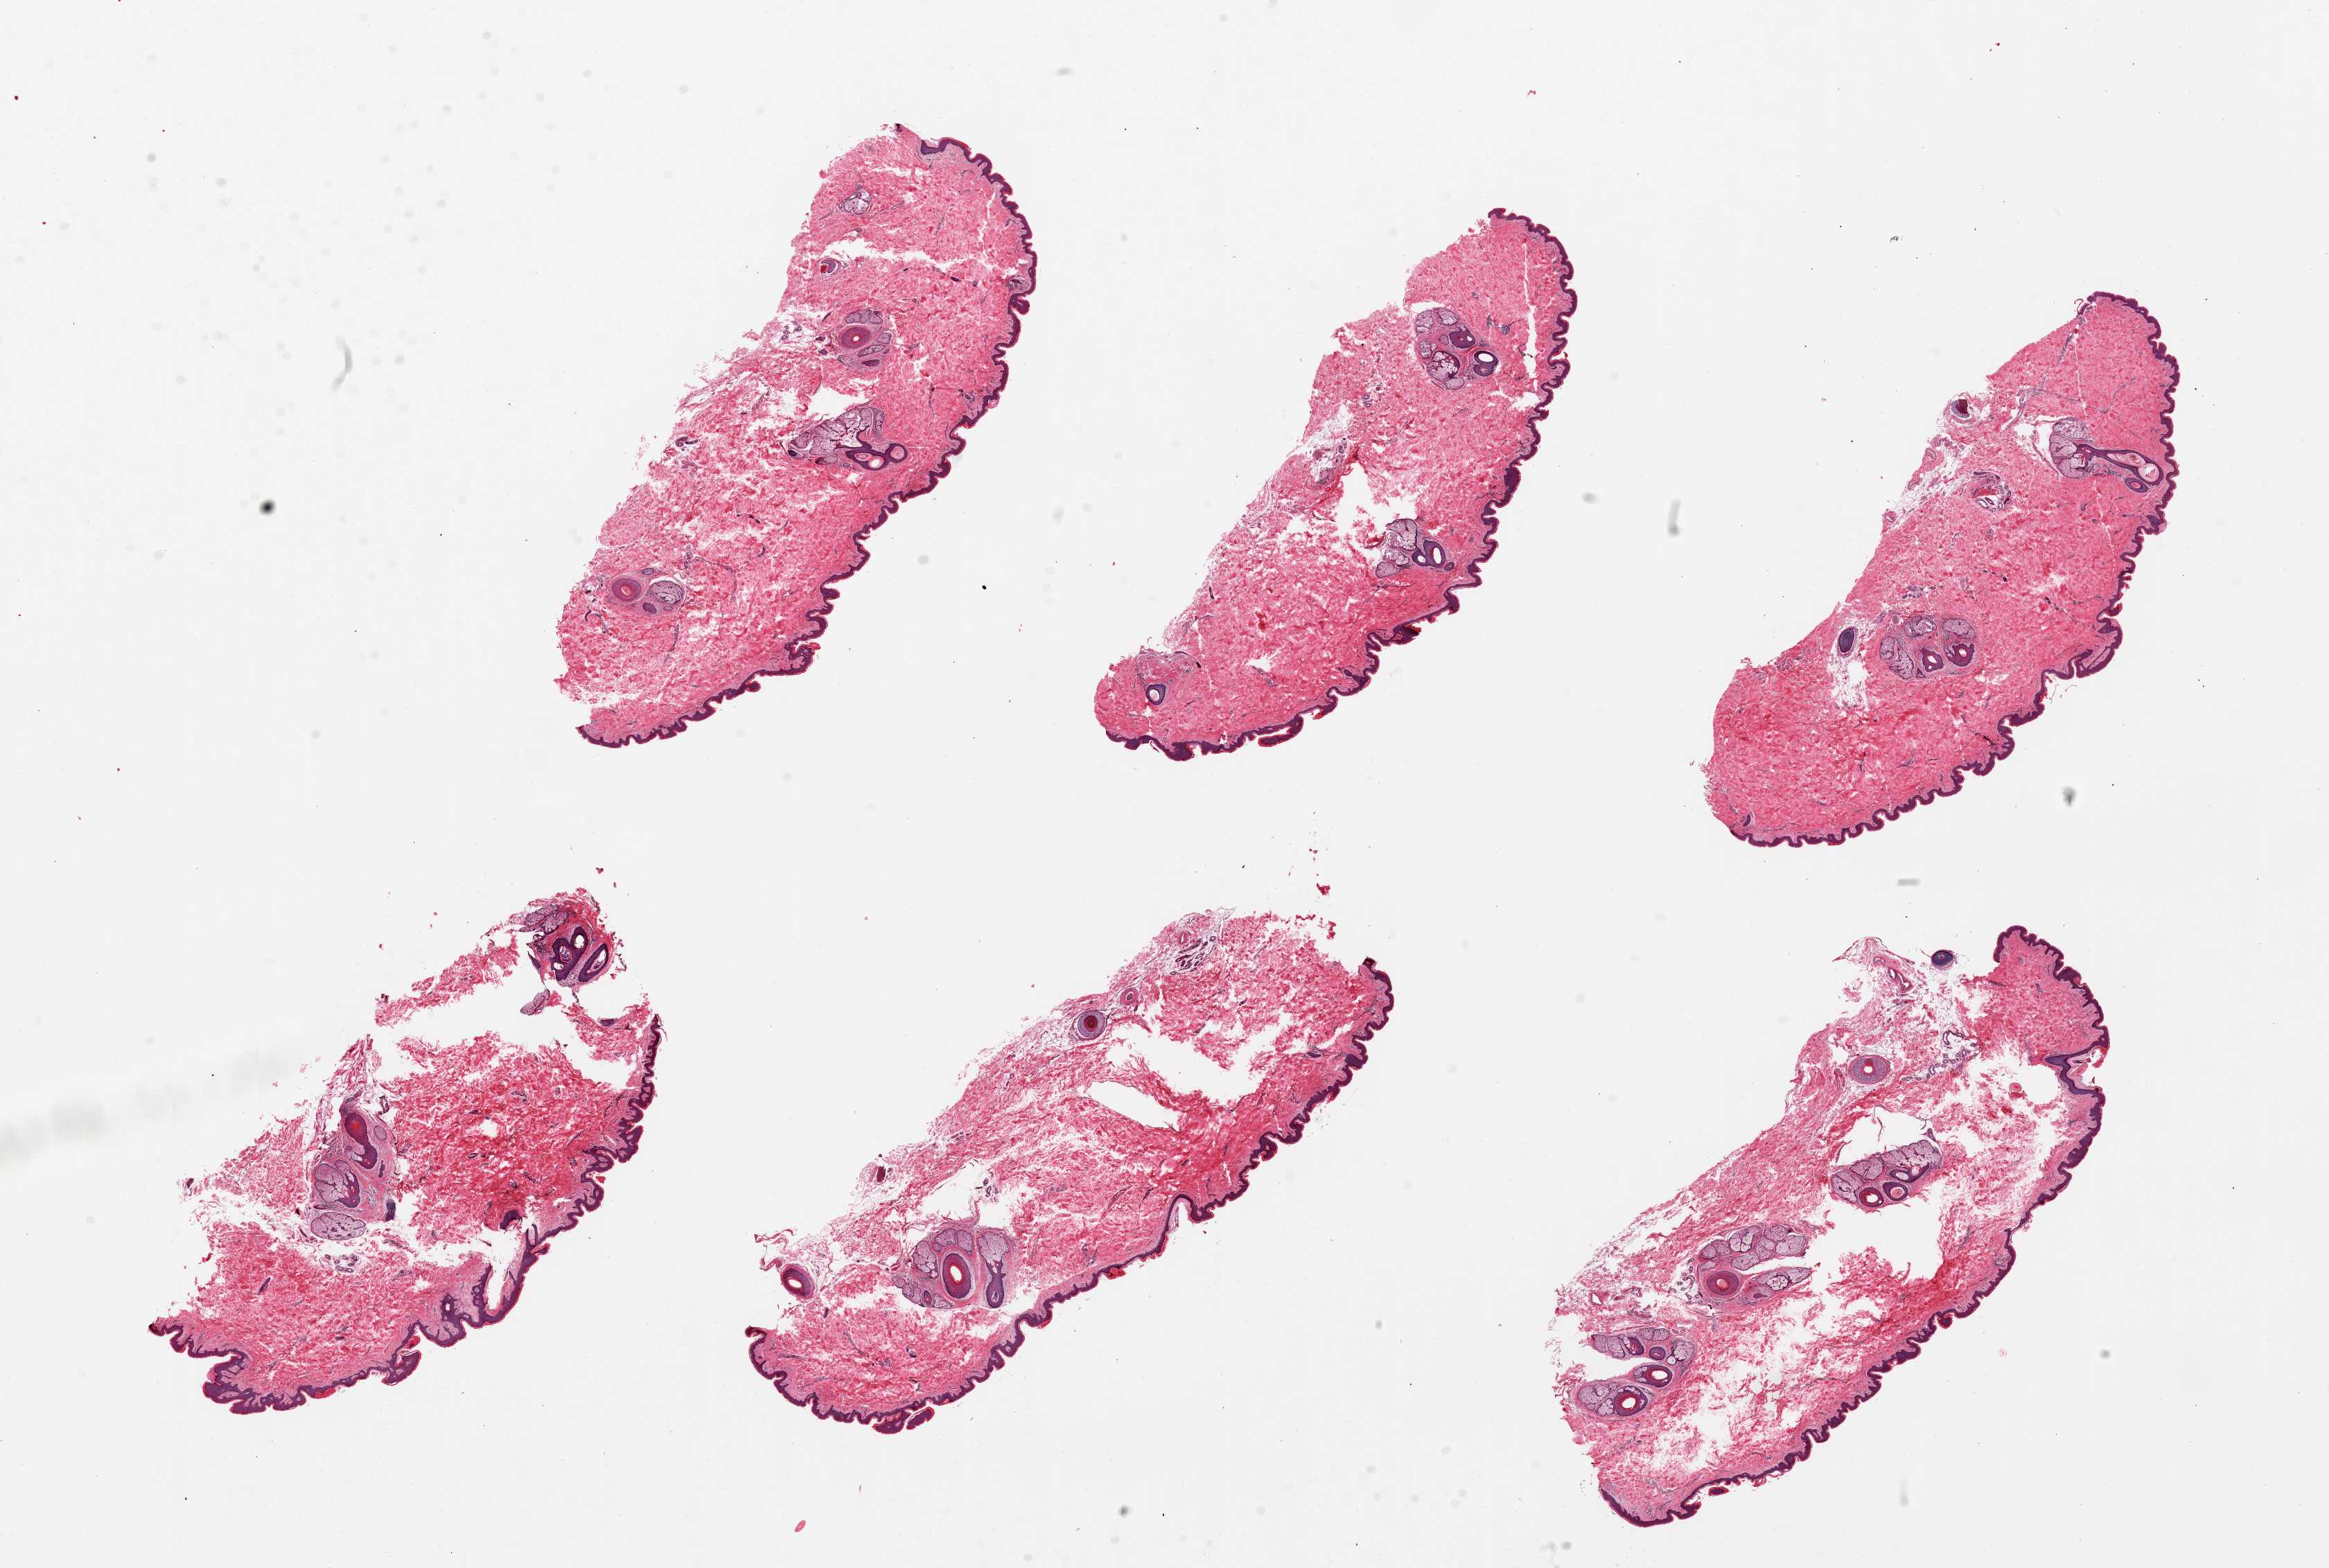
Digitized H&E-stained section — low-resolution overview of the scanned area, about 26.6 x 17.9 mm (acquisition: 20x scan), PAXgene-fixed paraffin-embedded (PFPE) section, sampled site (target tissue): skin of suprapubic region, donor tissue sample. Male donor.
Reviewer comment on this tissue sample: 6 pieces, up to 8x3mm; squmaous epithelium is ~1.5% thickness.